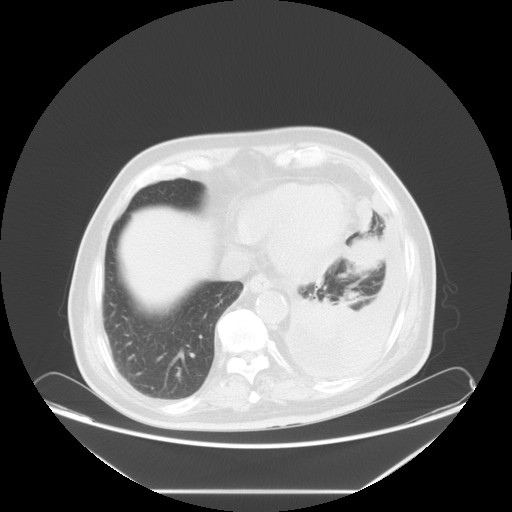
Chest CT, one axial slice. Slice 19 of 63 in the series (ordered by position). Reconstruction kernel STANDARD. Lung window (W 1500 / L -600 HU). 5 mm slice thickness. 512 × 512 image matrix, field of view 448 × 448 mm. Patient: male, 67 years. Case-level facts recorded for this patient, not image findings: clinical TNM (as recorded): T1b N1 M1a; histopathological grade: G3.
Structures marked on this image (bounding box drawn by a radiologist):
- lung tumour (recorded histology: small cell carcinoma): box from (x=342, y=232) to (x=388, y=280) px